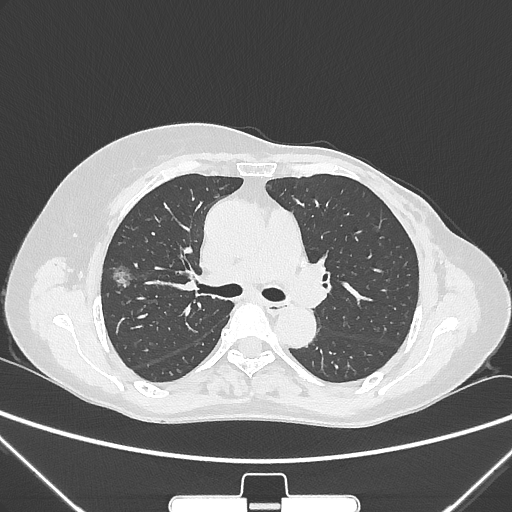
Chest CT, one axial slice. Slice 159 of 265 in the series (ordered by position). Reconstruction kernel IMR1,SharpPlus. 120 kVp. Lung window (W 1500 / L -600 HU). 512 × 512 image matrix, field of view 350 × 350 mm. Female patient, age 64 years. Case-level facts recorded for this patient, not image findings: clinical TNM (as recorded): T1c N0 M0; histopathological grade: G1-2.
Outlined on this slice (rectangle marked by the reading radiologist):
- lung tumour (recorded histology: adenocarcinoma): box from (x=110, y=263) to (x=137, y=298) px